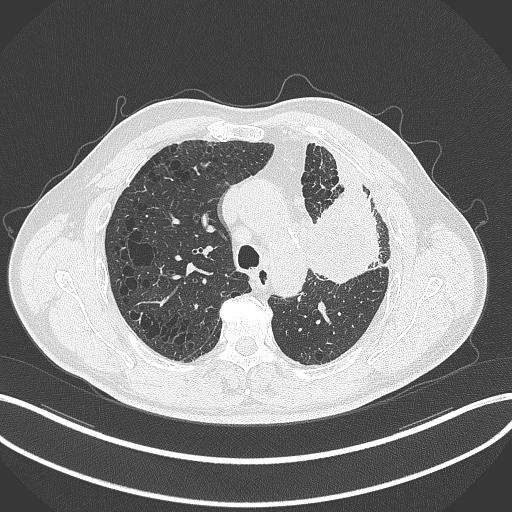
Chest CT, one axial slice; position 220 of 297 along the scan axis; reconstruction kernel B70f; 120 kVp; lung window (W 1500 / L -600 HU); 1 mm slice thickness; 512 × 512 image matrix. Male patient, age 68 years. From the clinical record (not read from this slice): clinical TNM (as recorded): T3 N3 M1.
Outlined on this slice (rectangle marked by the reading radiologist):
- lung tumour (recorded histology: adenocarcinoma): bounding box <308,188,381,293> (left, top, right, bottom; pixels)